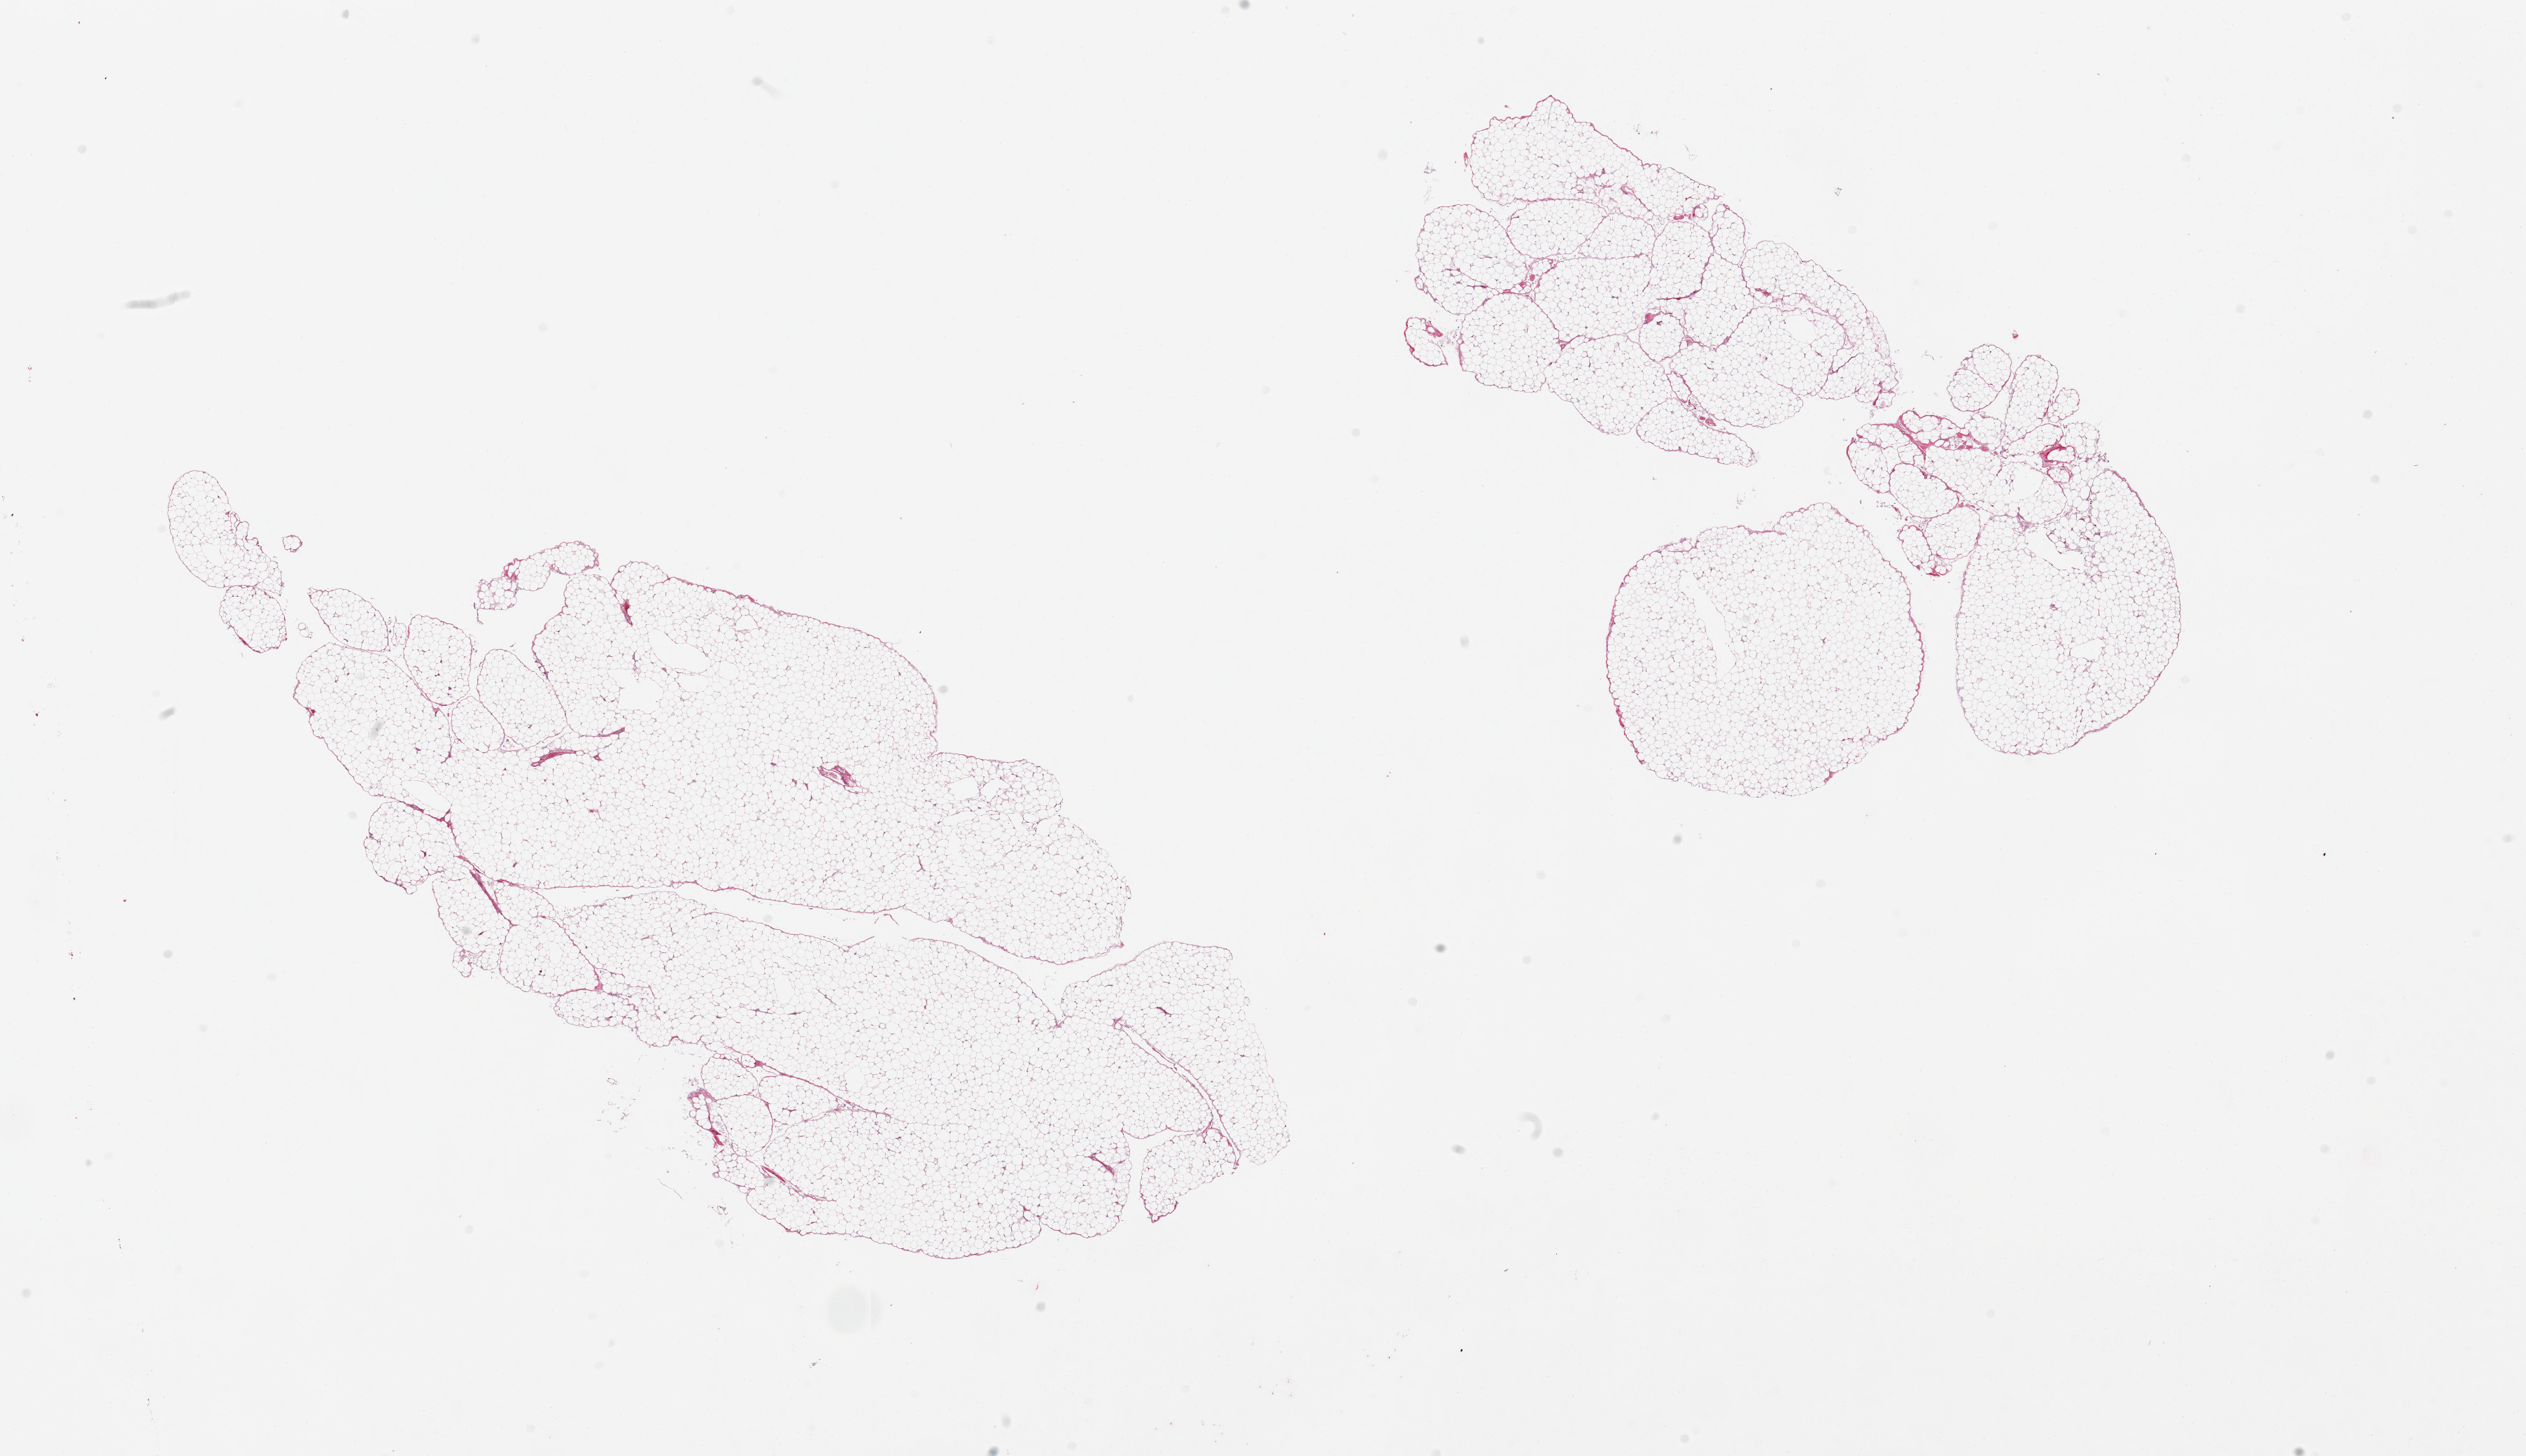
Hematoxylin and eosin (H&E) whole-slide image, brightfield, low-resolution overview of the scanned area, about 28.5 x 16.5 mm, PAXgene-fixed paraffin-embedded (PFPE) section, sampled site (target tissue): omentum, donor tissue sample.
Review note (as recorded): 2 pieces, minimal fibrous/vascular componenet; good specimens.